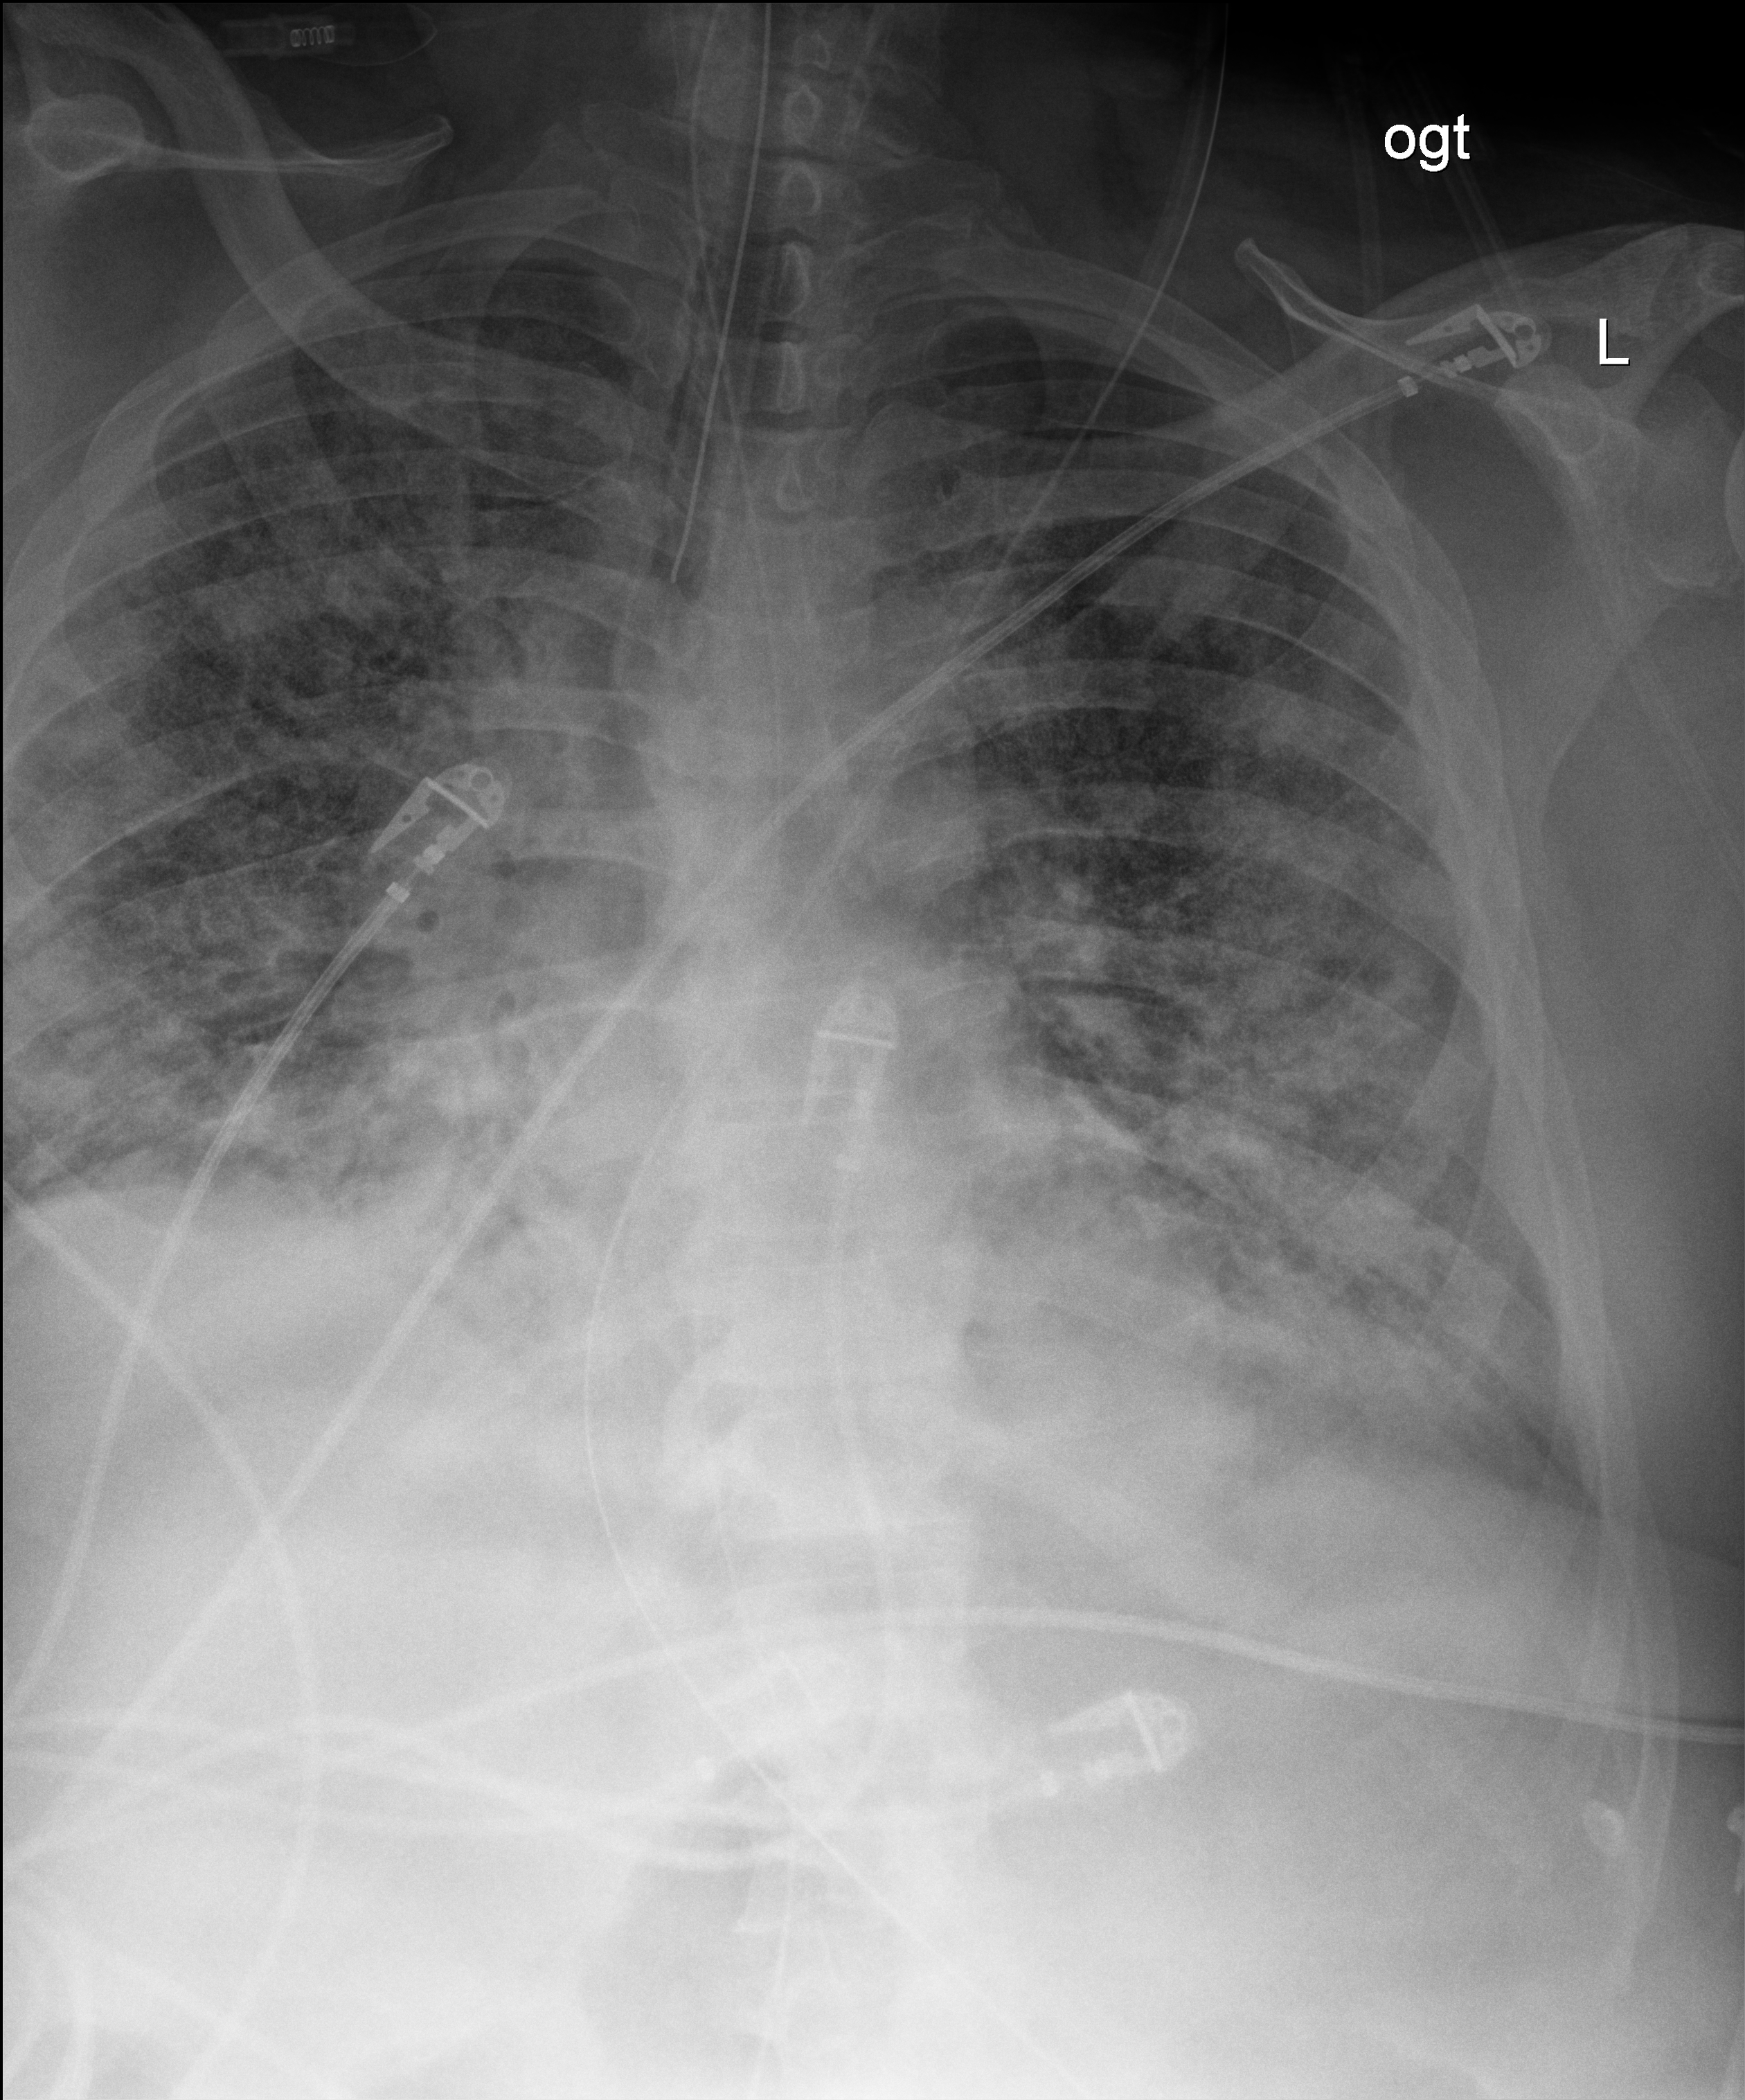
Portable chest radiograph; anteroposterior (AP) projection. Male patient hospitalised with COVID-19, age 60–74 years.
Admission-level facts for this patient (not findings on this image; timing relative to this image not recorded):
- diabetes (admission record): yes
- COPD (admission record): no
- admitted to intensive care during this hospital stay: yes